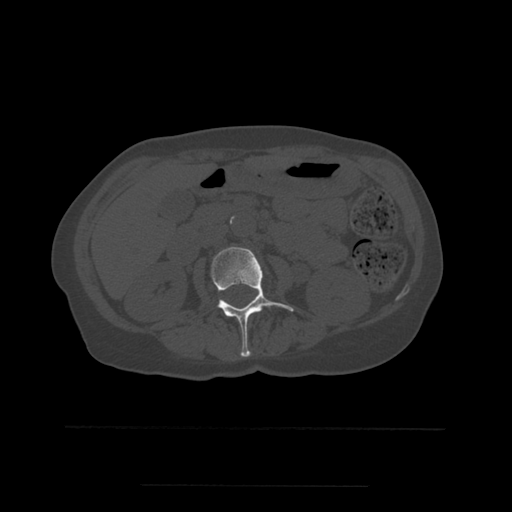
CT including the spine, one axial slice; position 210 of 544 along the scan axis; bone window (W 1800 / L 400 HU); 1.25 mm slice thickness; 512 × 512 image matrix, field of view 350 × 350 mm. Patient age 58 years. From the clinical record (not read from this slice): primary cancer: lung.
Structures marked on this image (semi-automatically segmented with operator editing):
- L2 vertebra: bounding box (x1, y1, x2, y2) in pixels: (211, 247, 294, 357)